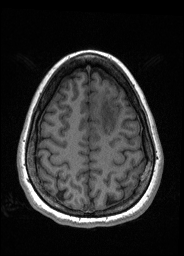
Pre-operative brain MRI before brain-tumour surgery, one axial slice; slice 53 of 176 in the series (ordered by position); T1-weighted post-contrast; 1 mm slice thickness; 184 × 256 image matrix, field of view 180 × 250 mm. Case-level facts recorded for this patient, not image findings: histopathology: Oligodendroglioma; WHO grade: 2; IDH mutation: yes.
Structures marked on this image (expert manual segmentation):
- tumour: bounding box [x1, y1, x2, y2] px = [91, 96, 118, 135]